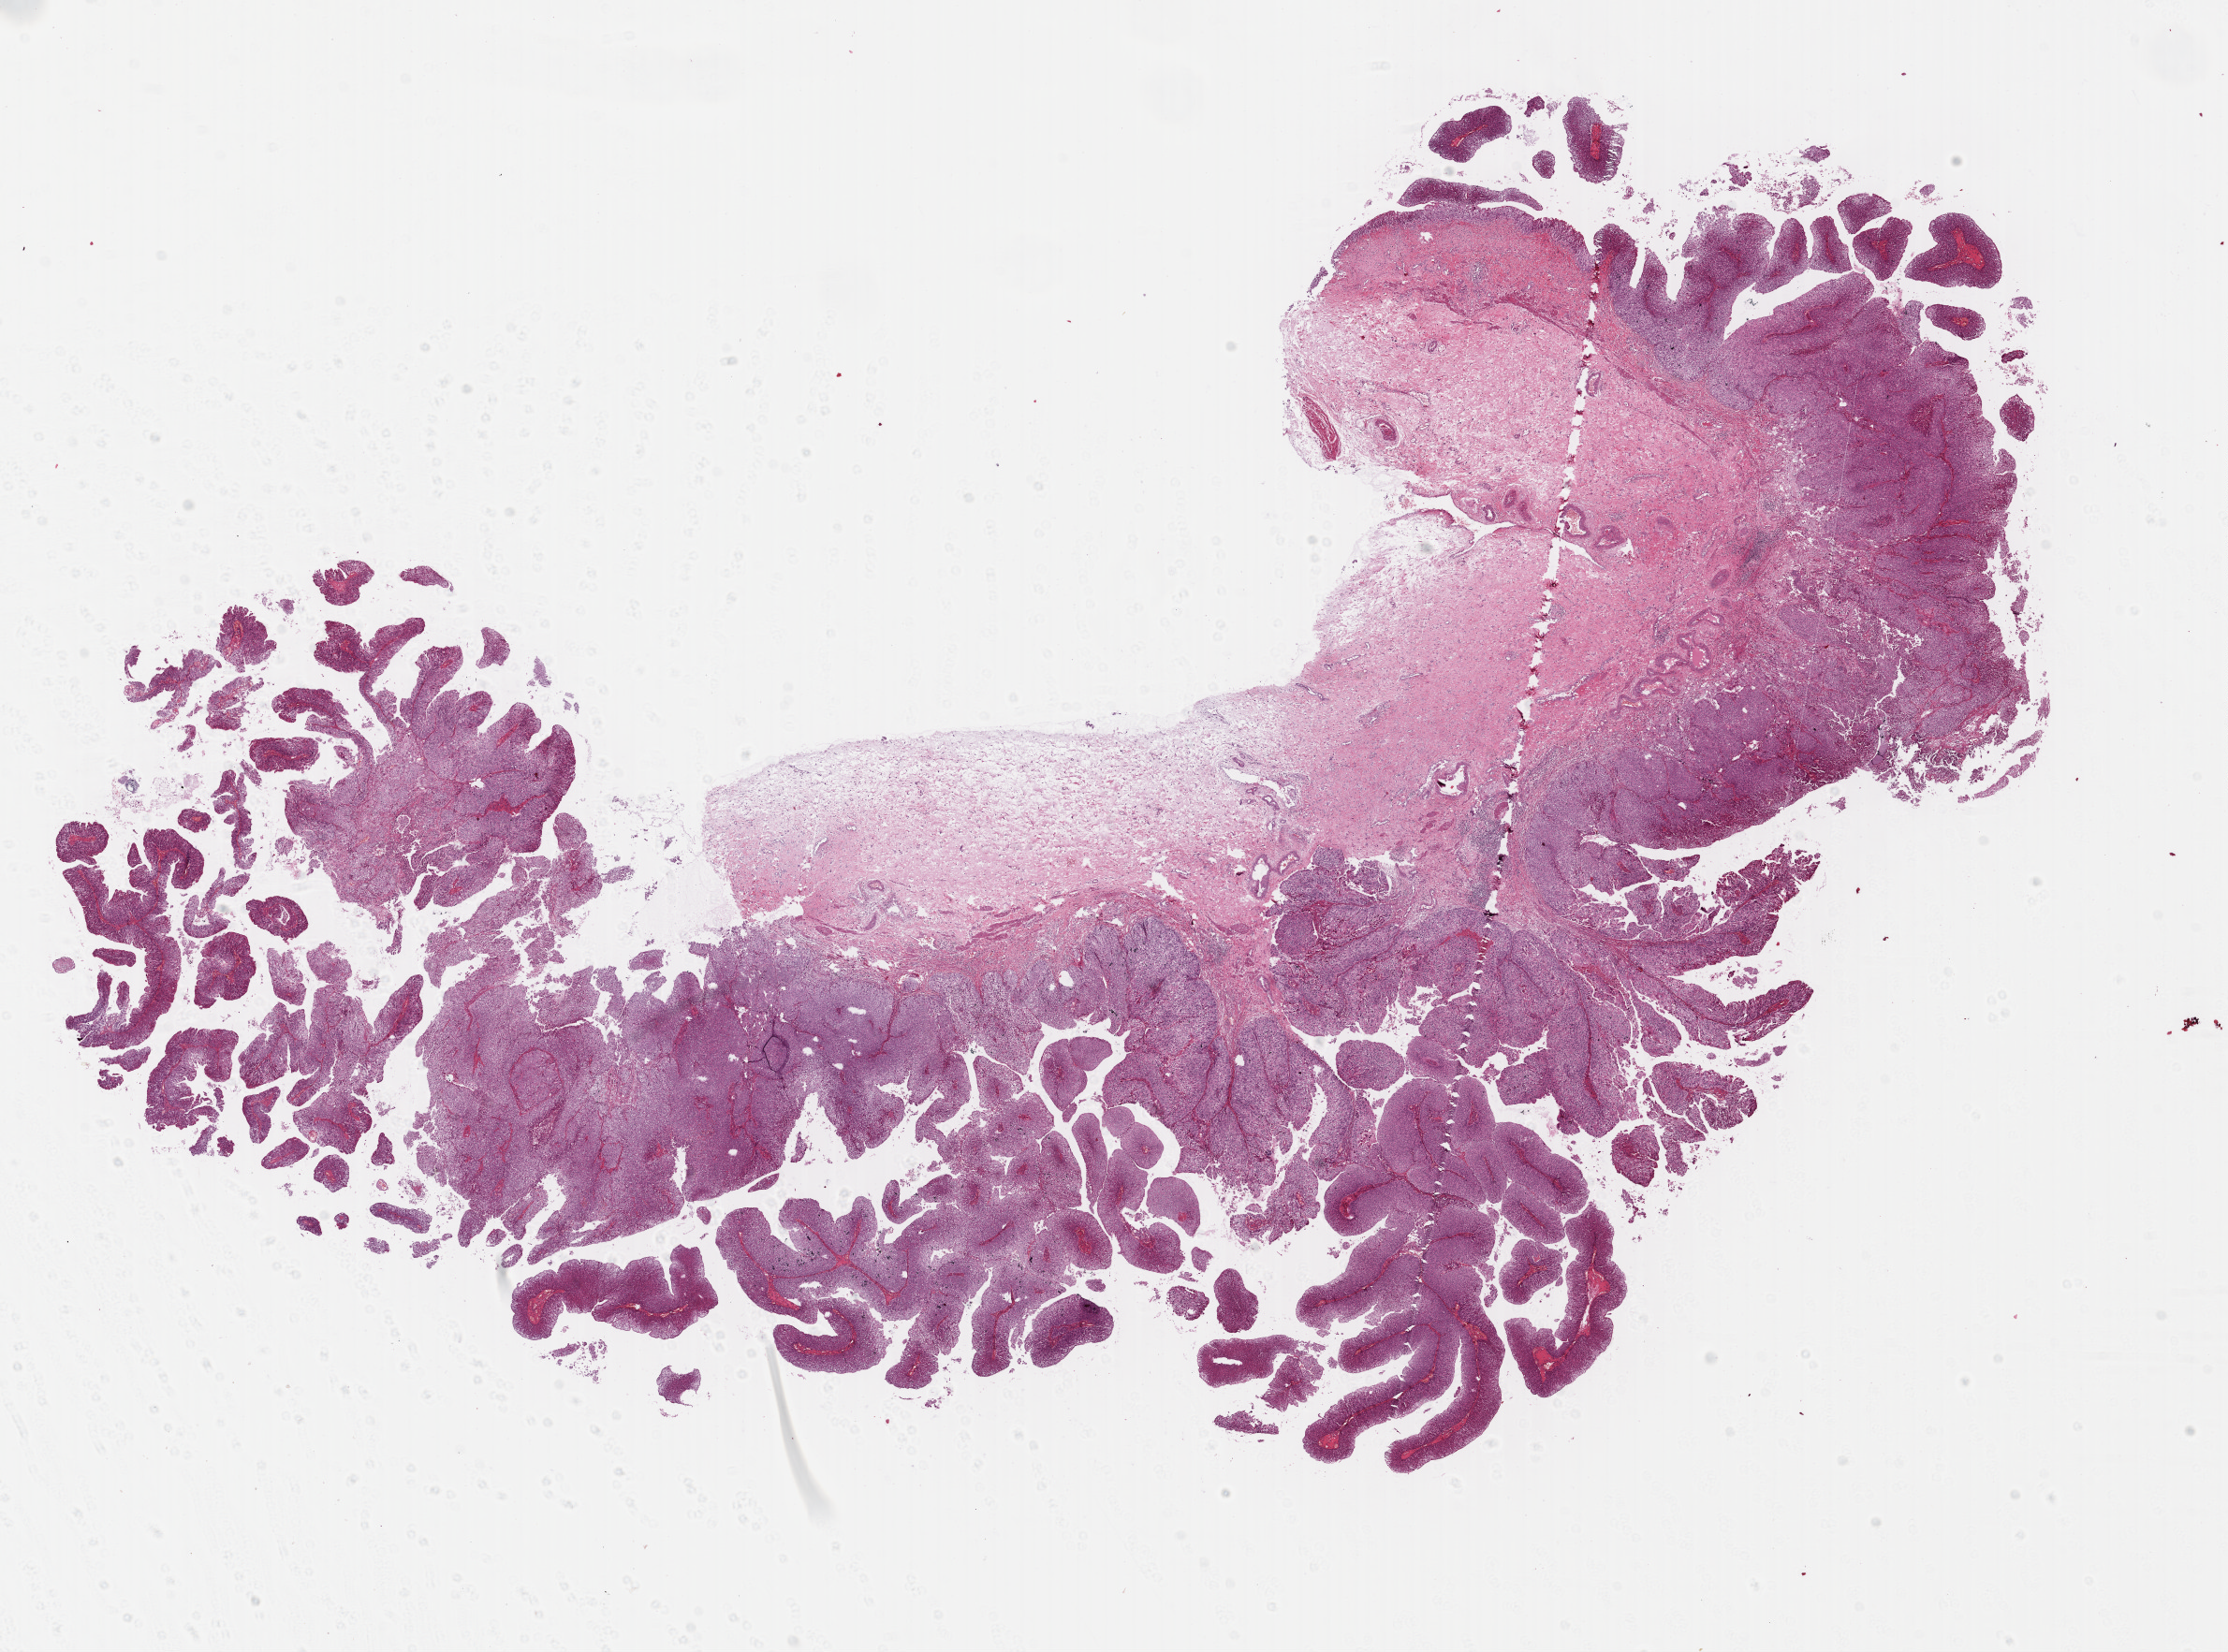
Hematoxylin and eosin (H&E) stained whole-slide image — shown as a low-resolution overview of the whole scanned area (about 18.7 x 13.9 mm, slide scanned at 40x). Formalin-fixed paraffin-embedded (FFPE) diagnostic section. Bladder, primary tumour sample. Male, age 48 years at initial diagnosis. Histologic grade: low grade.
Histologic diagnosis: Papillary transitional cell carcinoma. AJCC pathologic stage: II (7th edition).